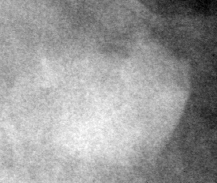
Crop from a digitized film mammogram around one marked abnormality, left breast, CC view.
- Mass, shape irregular, margins circumscribed / obscured; BI-RADS assessment category 4; subtlety rating 3 on a 1 (subtle) to 5 (obvious) scale; pathology (as recorded): benign.